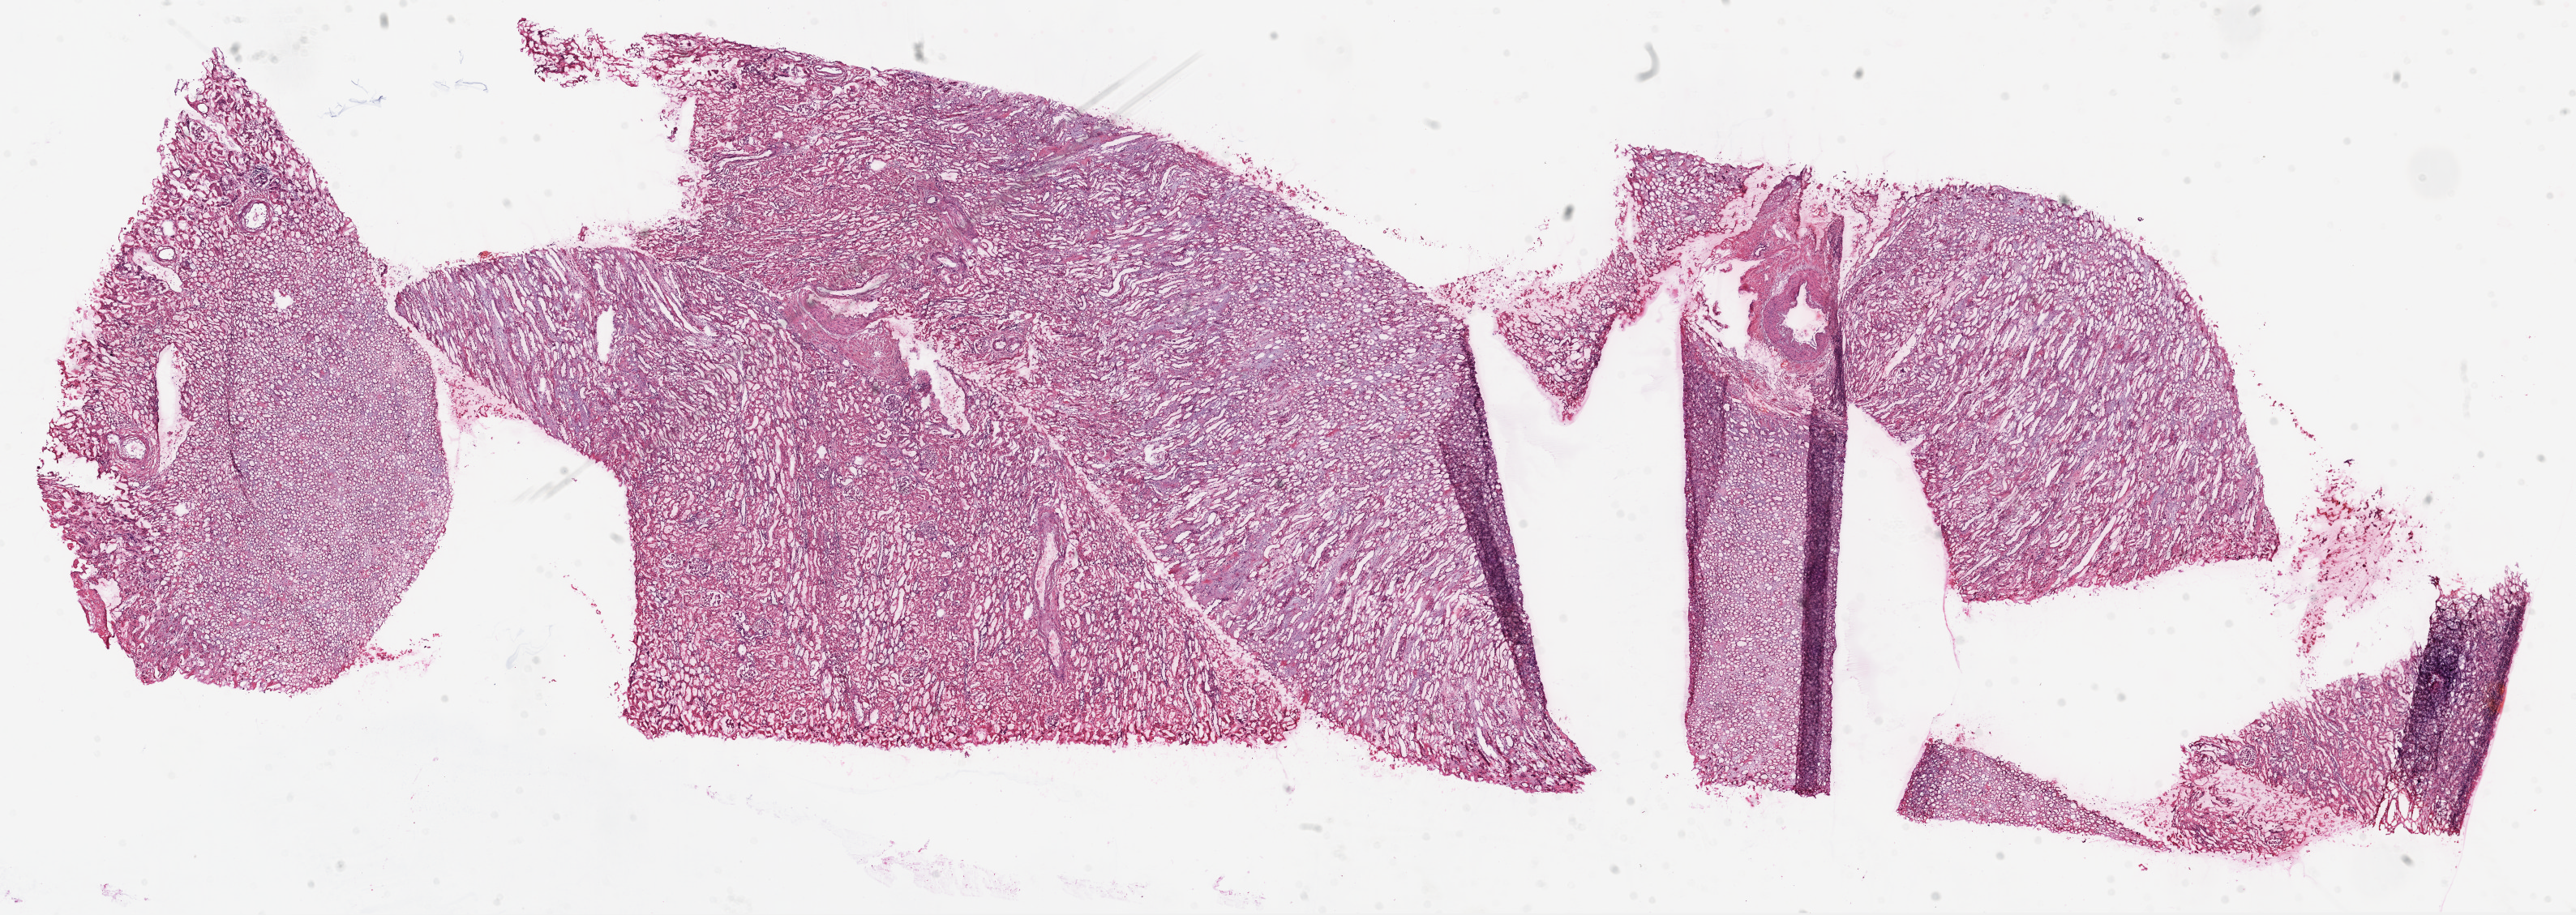
Digitized H&E-stained tissue section (whole slide), low-resolution overview of the scanned area, about 25.6 x 9.1 mm (from a 20x scan). Frozen section from the top of the tissue portion. Solid tissue normal (non-tumour tissue) sample from the kidney. Patient sex: male.
This section: solid tissue normal sample (biorepository sample class). Patient diagnosis: Clear cell adenocarcinoma, NOS.